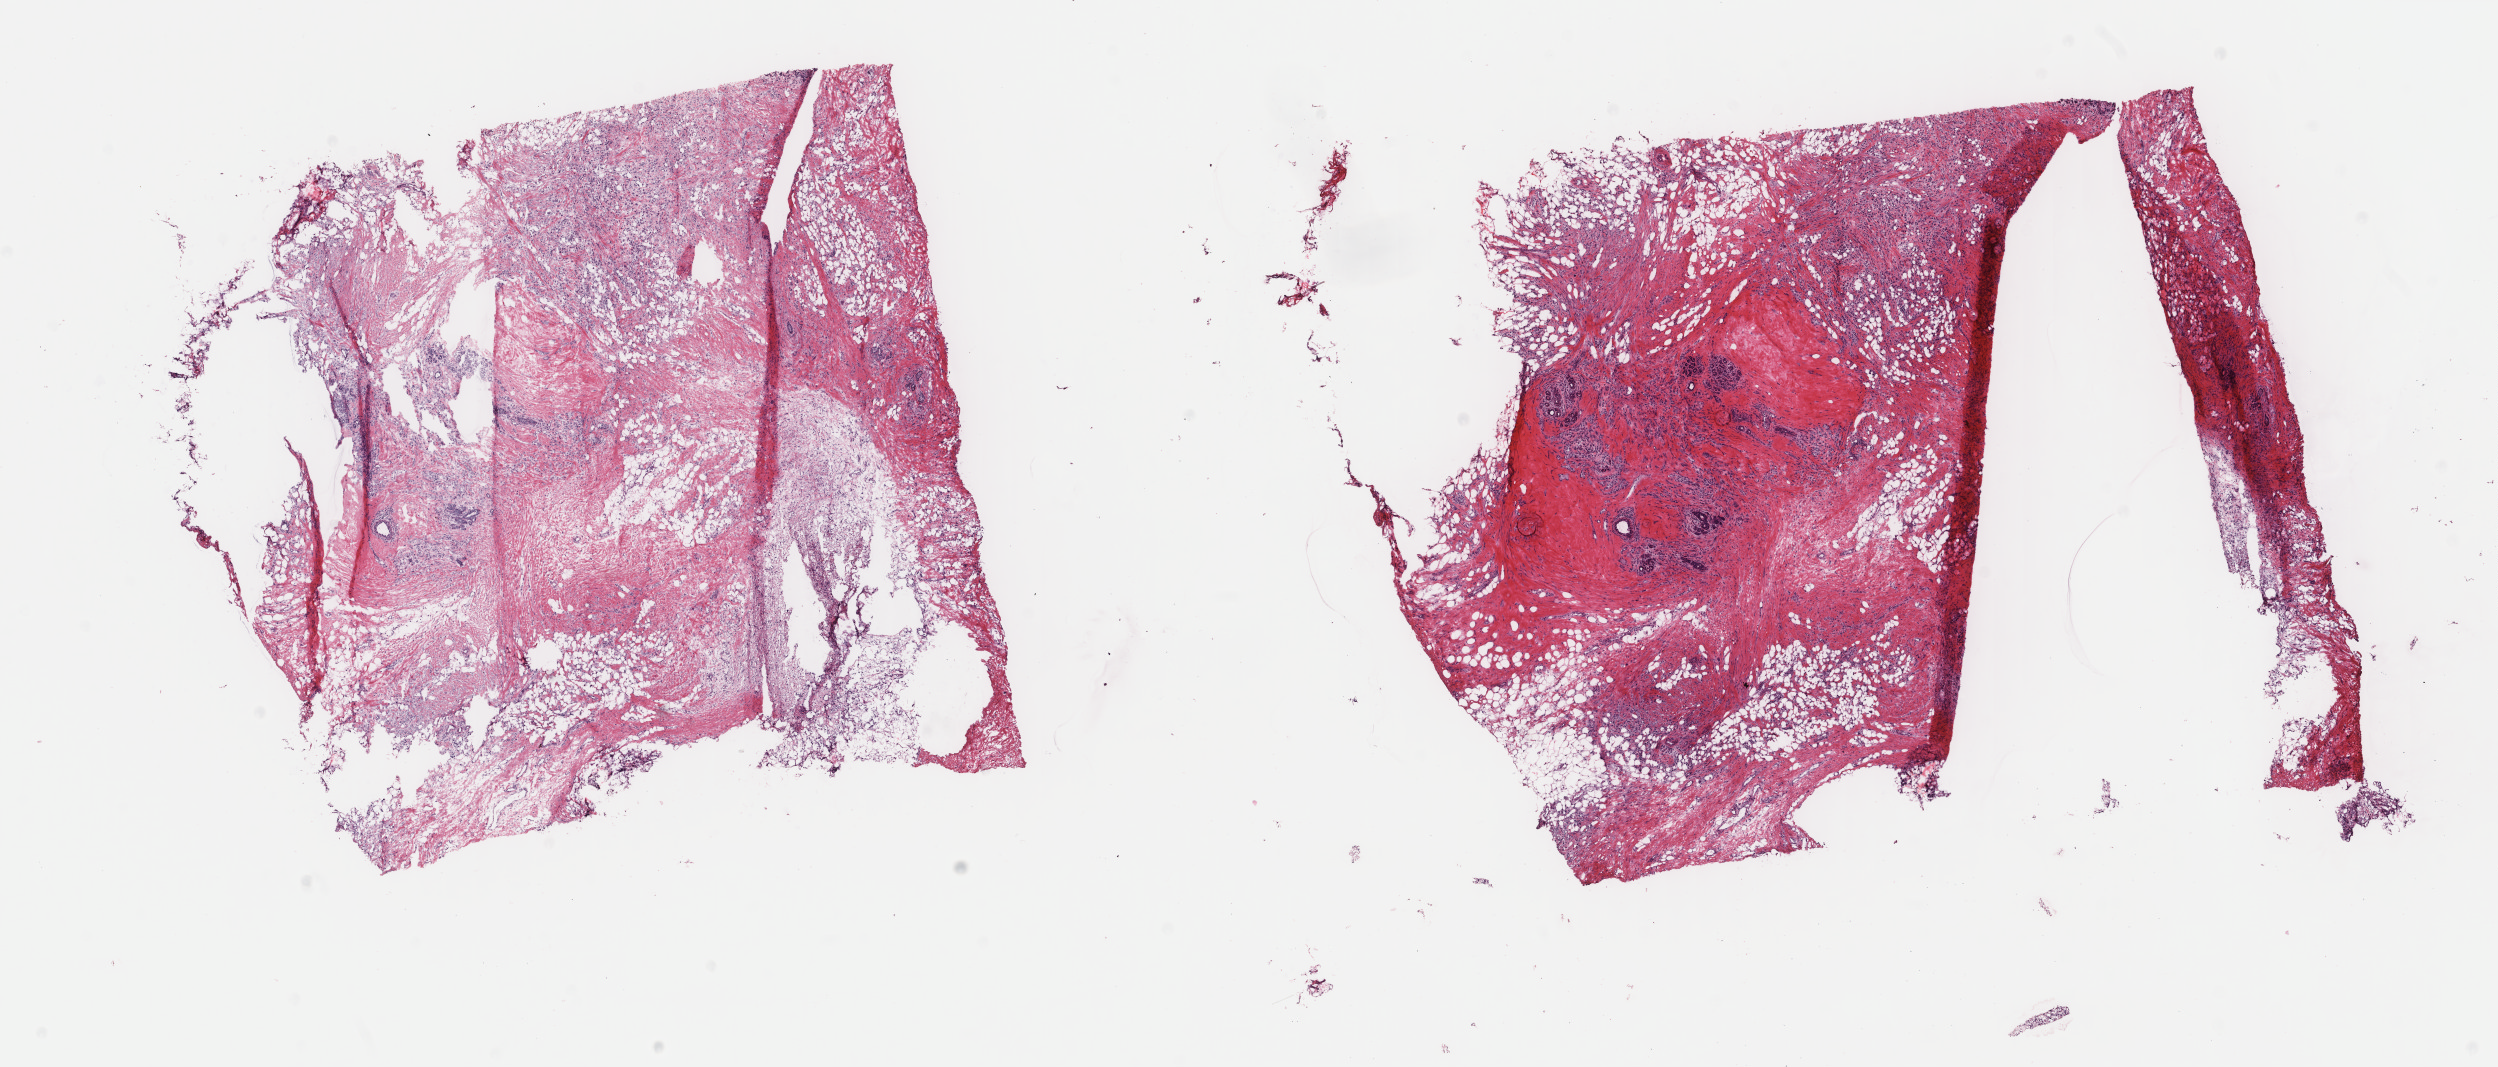
Whole-slide histology image, H&E-stained — whole scanned area (about 19.8 x 8.5 mm, acquisition: 40x scan) shown as a low-resolution overview. Frozen section. Sample: primary tumour, breast. Female patient; age at initial diagnosis 59 years. Composition of this section per pathologist review: tumour cells 40%, tumour nuclei 60%.
Diagnosis: Lobular carcinoma, NOS.